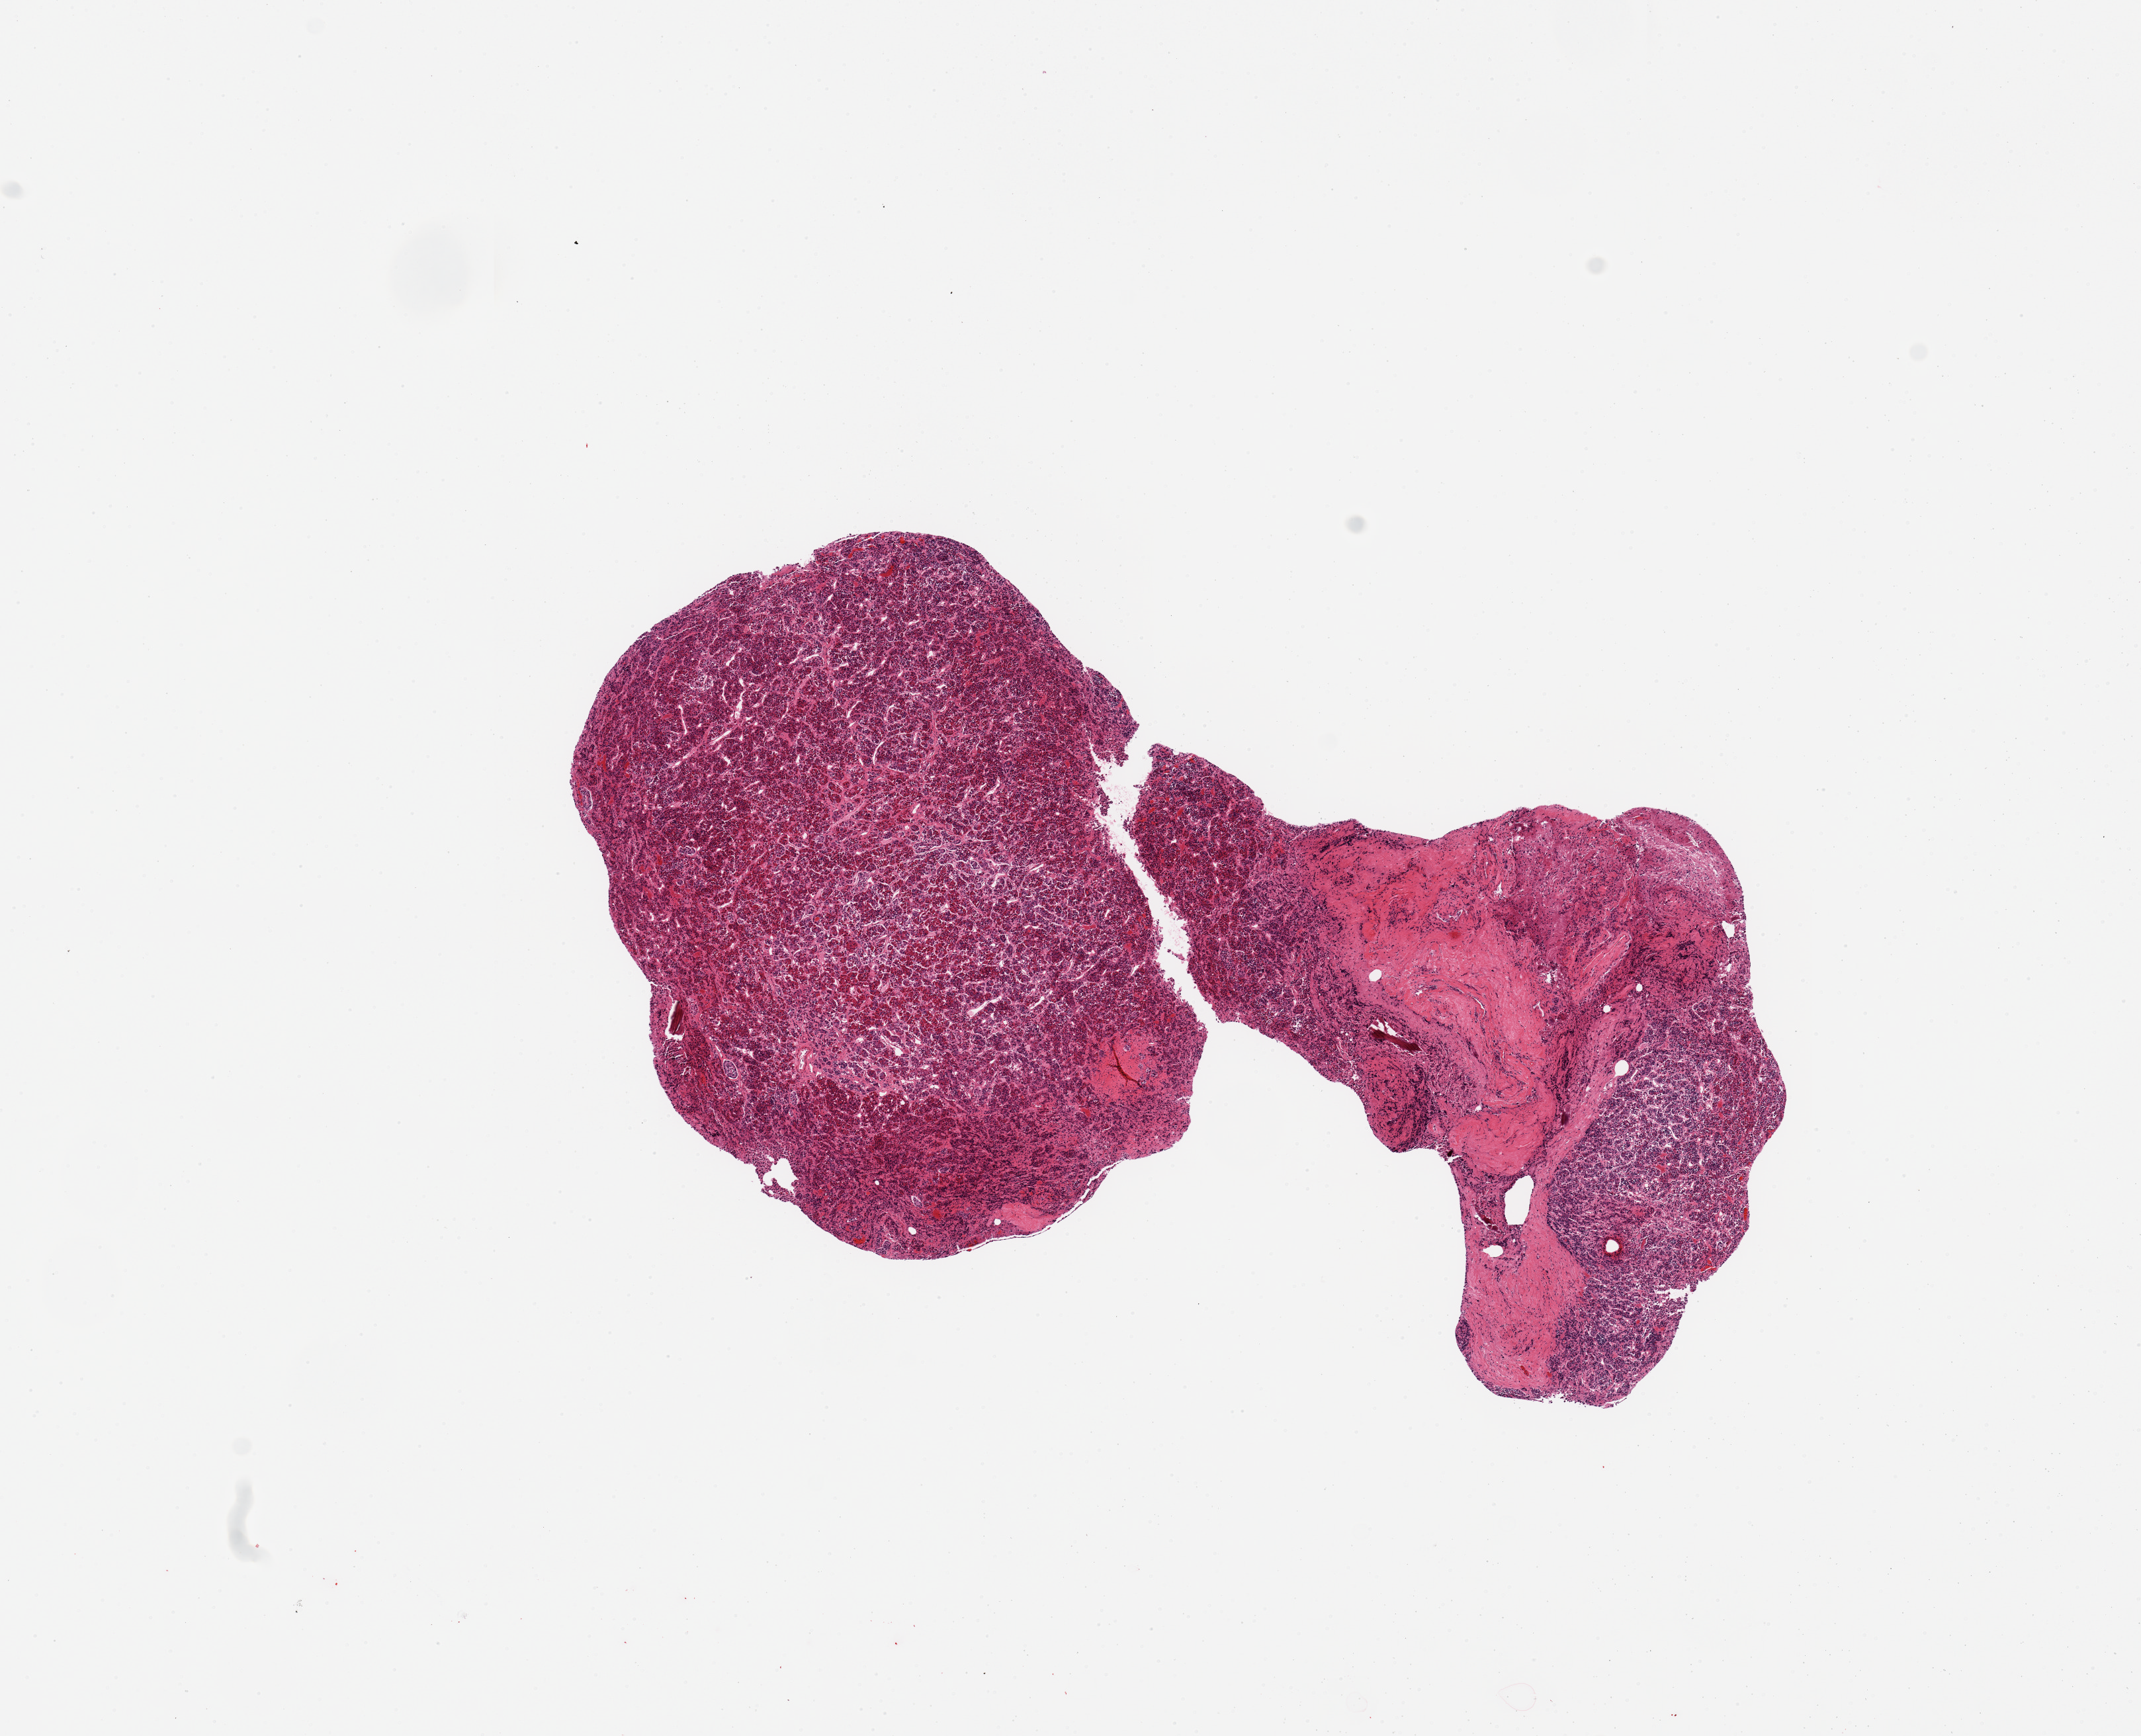
Haematoxylin and eosin whole-slide image, shown as a low-resolution overview of the whole scanned area (about 12.8 x 10.4 mm, acquisition: 20x scan), PAXgene-fixed paraffin-embedded (PFPE) section, section of pituitary (target tissue), tissue donor sample. Donor: male.
Review note (as recorded): 1 piece, adenohypophysis, 20% dura.